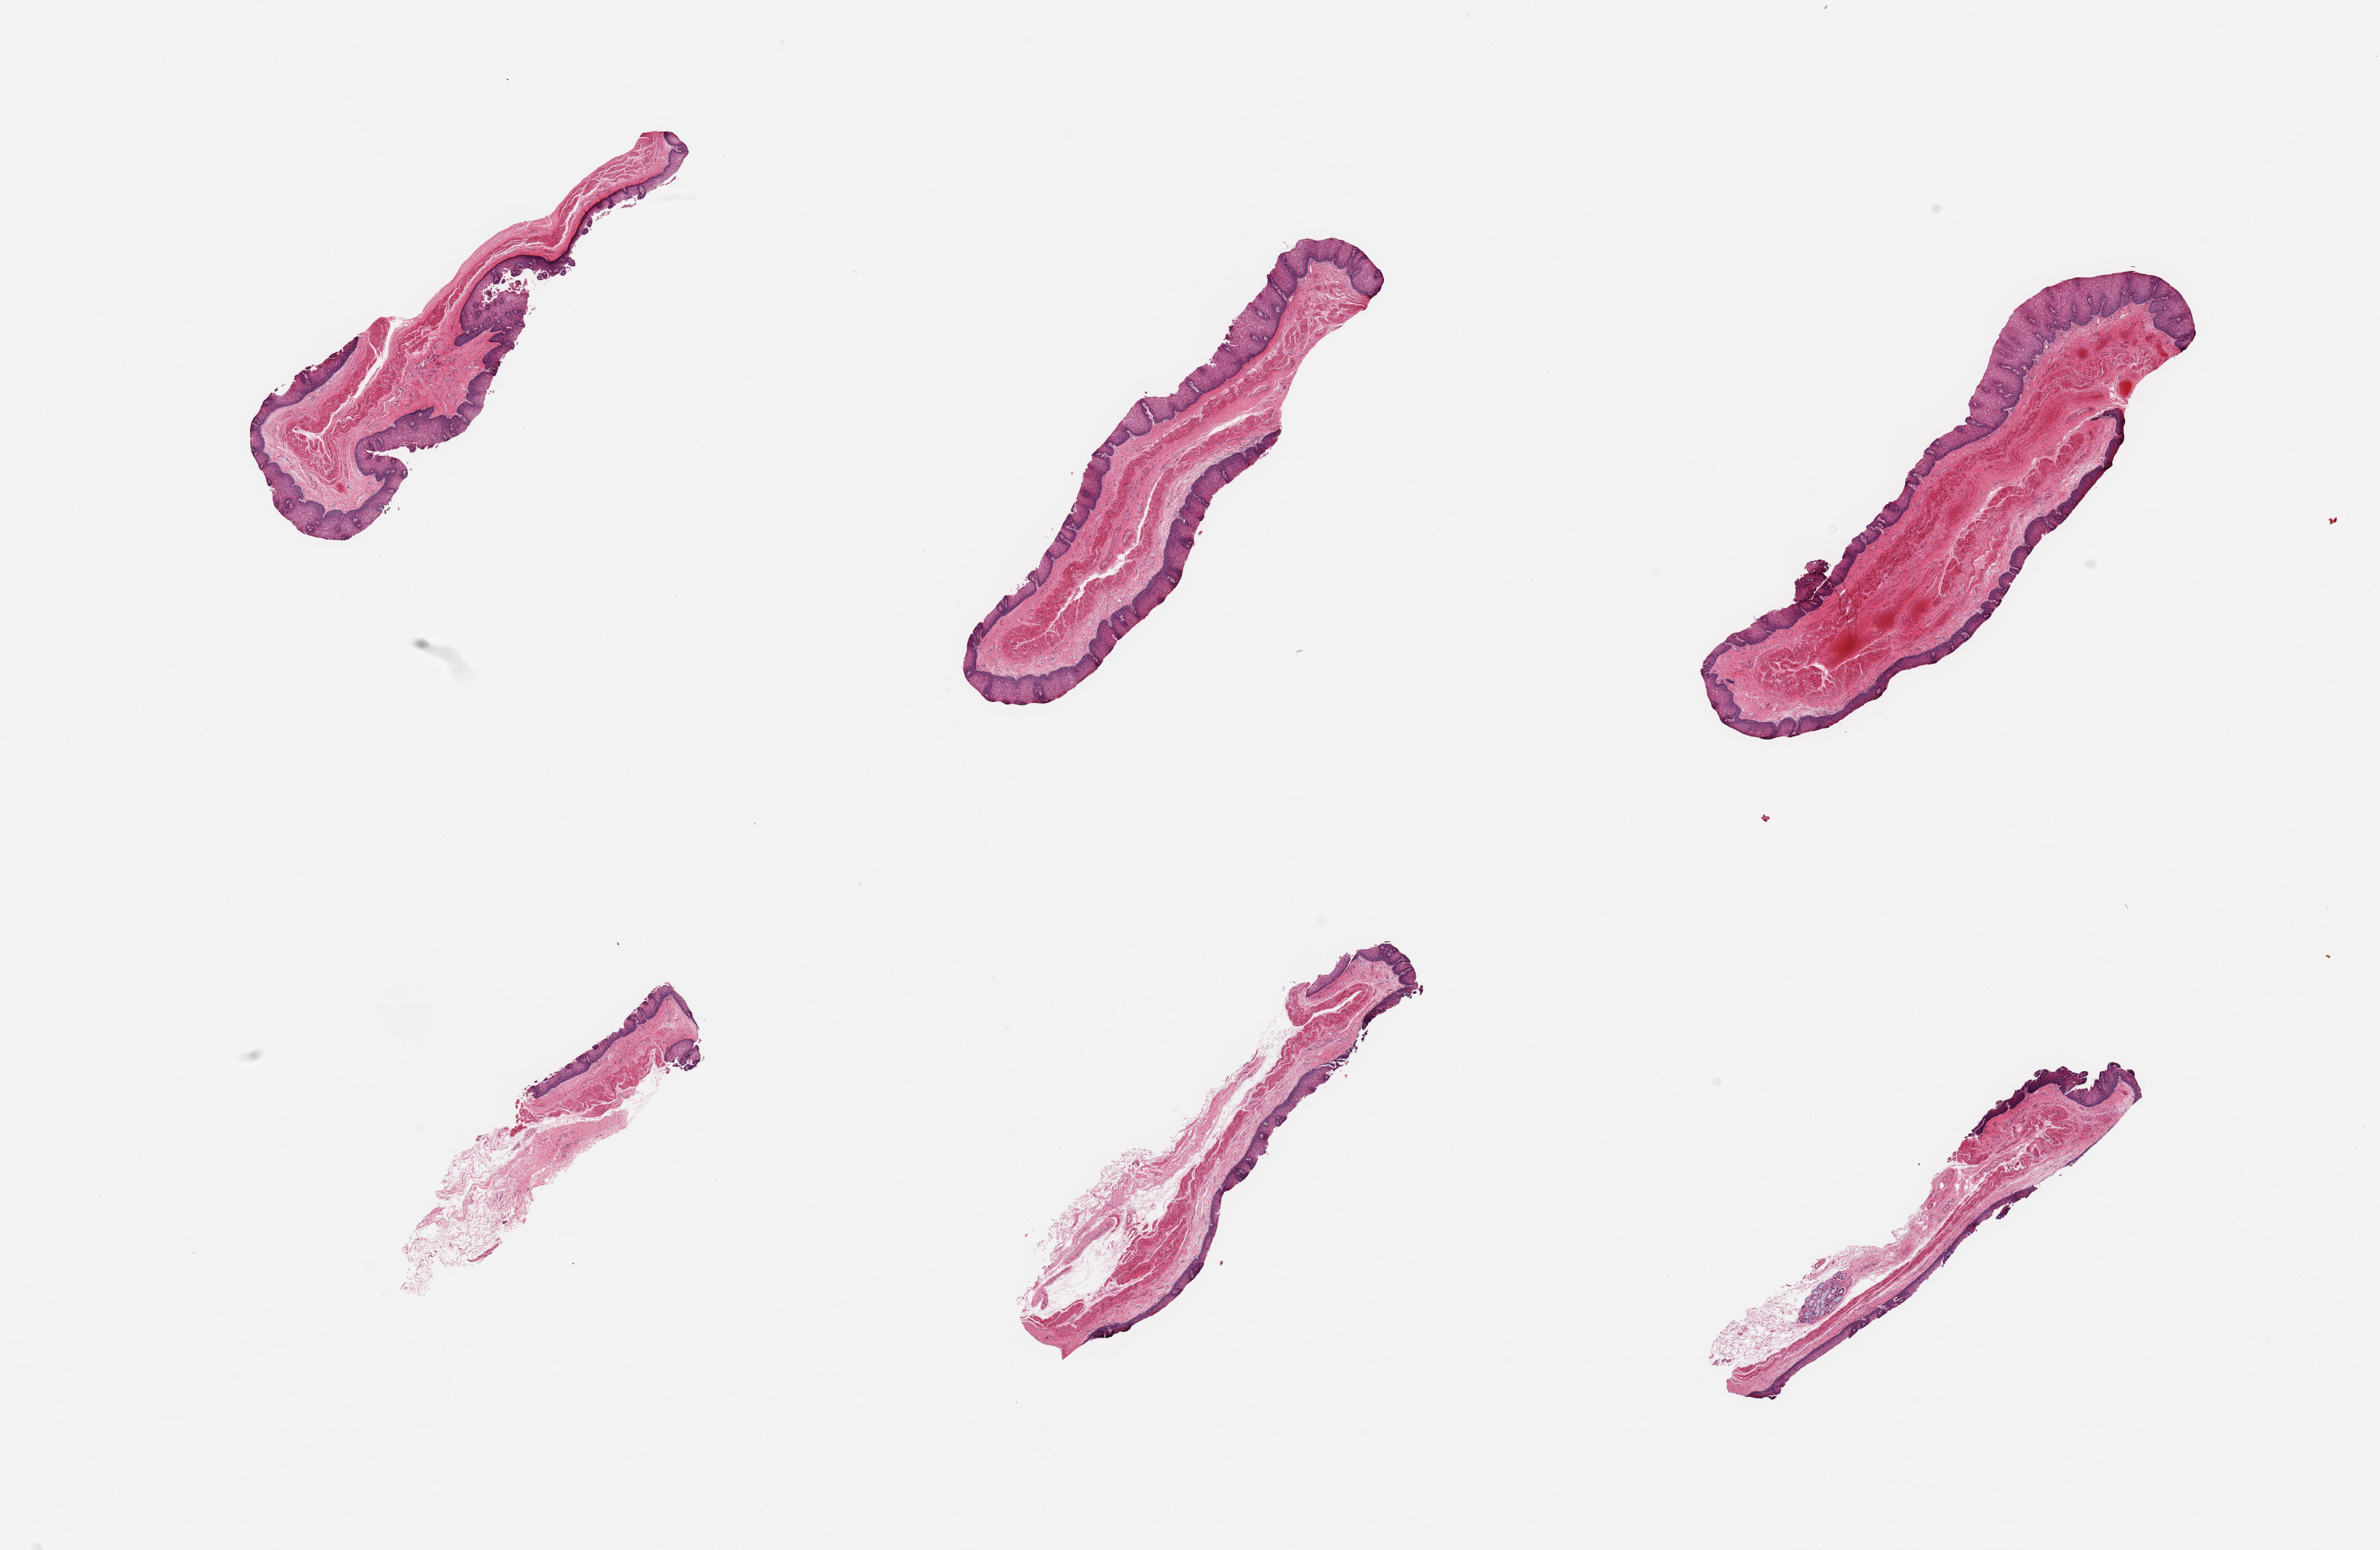
Digitized haematoxylin and eosin-stained section, a low-resolution overview of the entire scanned area, about 23.6 x 15.4 mm (from a 20x scan); PAXgene-fixed paraffin-embedded (PFPE) section; sampled site (target tissue): esophageal mucous membrane; tissue donor sample.
• reviewer comment on this tissue sample: 6 pieces, squamous mucosa is up to ~0.4mm, ~40-50% thickness